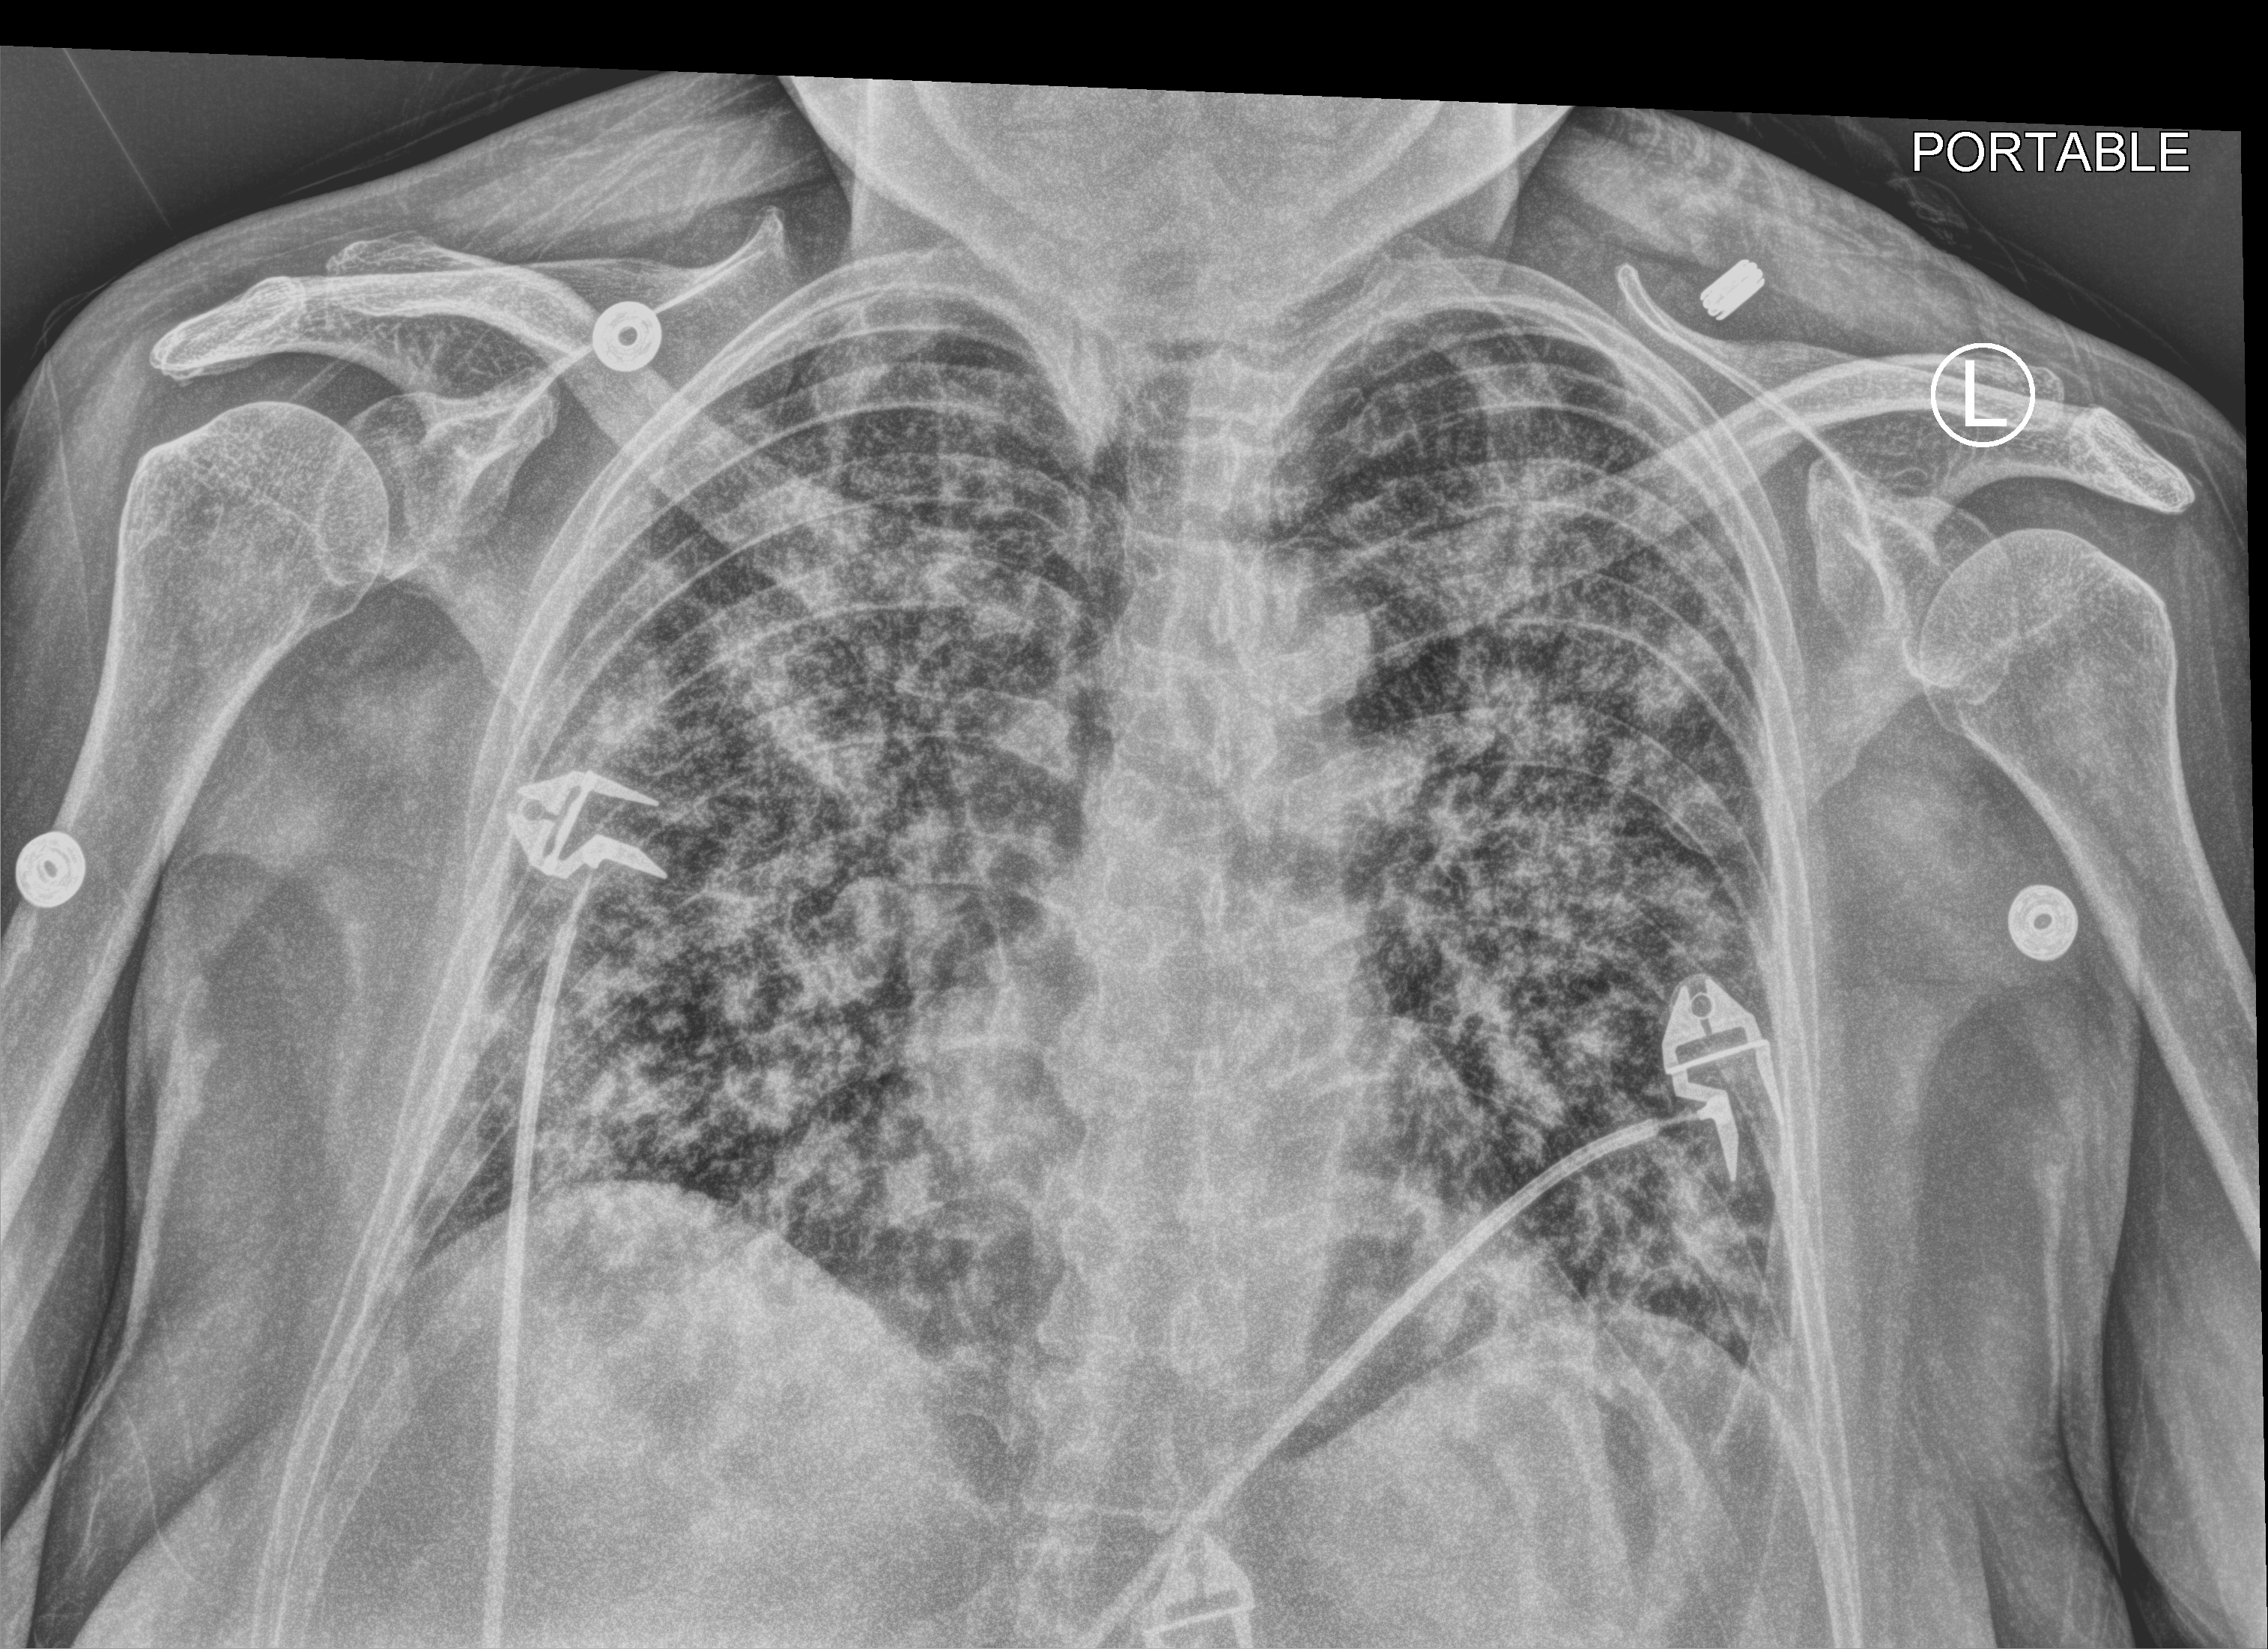
Portable chest radiograph; anteroposterior (AP) projection. Patient hospitalised with COVID-19; female, aged 60–74 years.
From the hospital-stay record, not from the radiograph (when in the stay this image was taken is not recorded): length of hospital stay: 16 days; mechanically ventilated during this hospital stay: no.